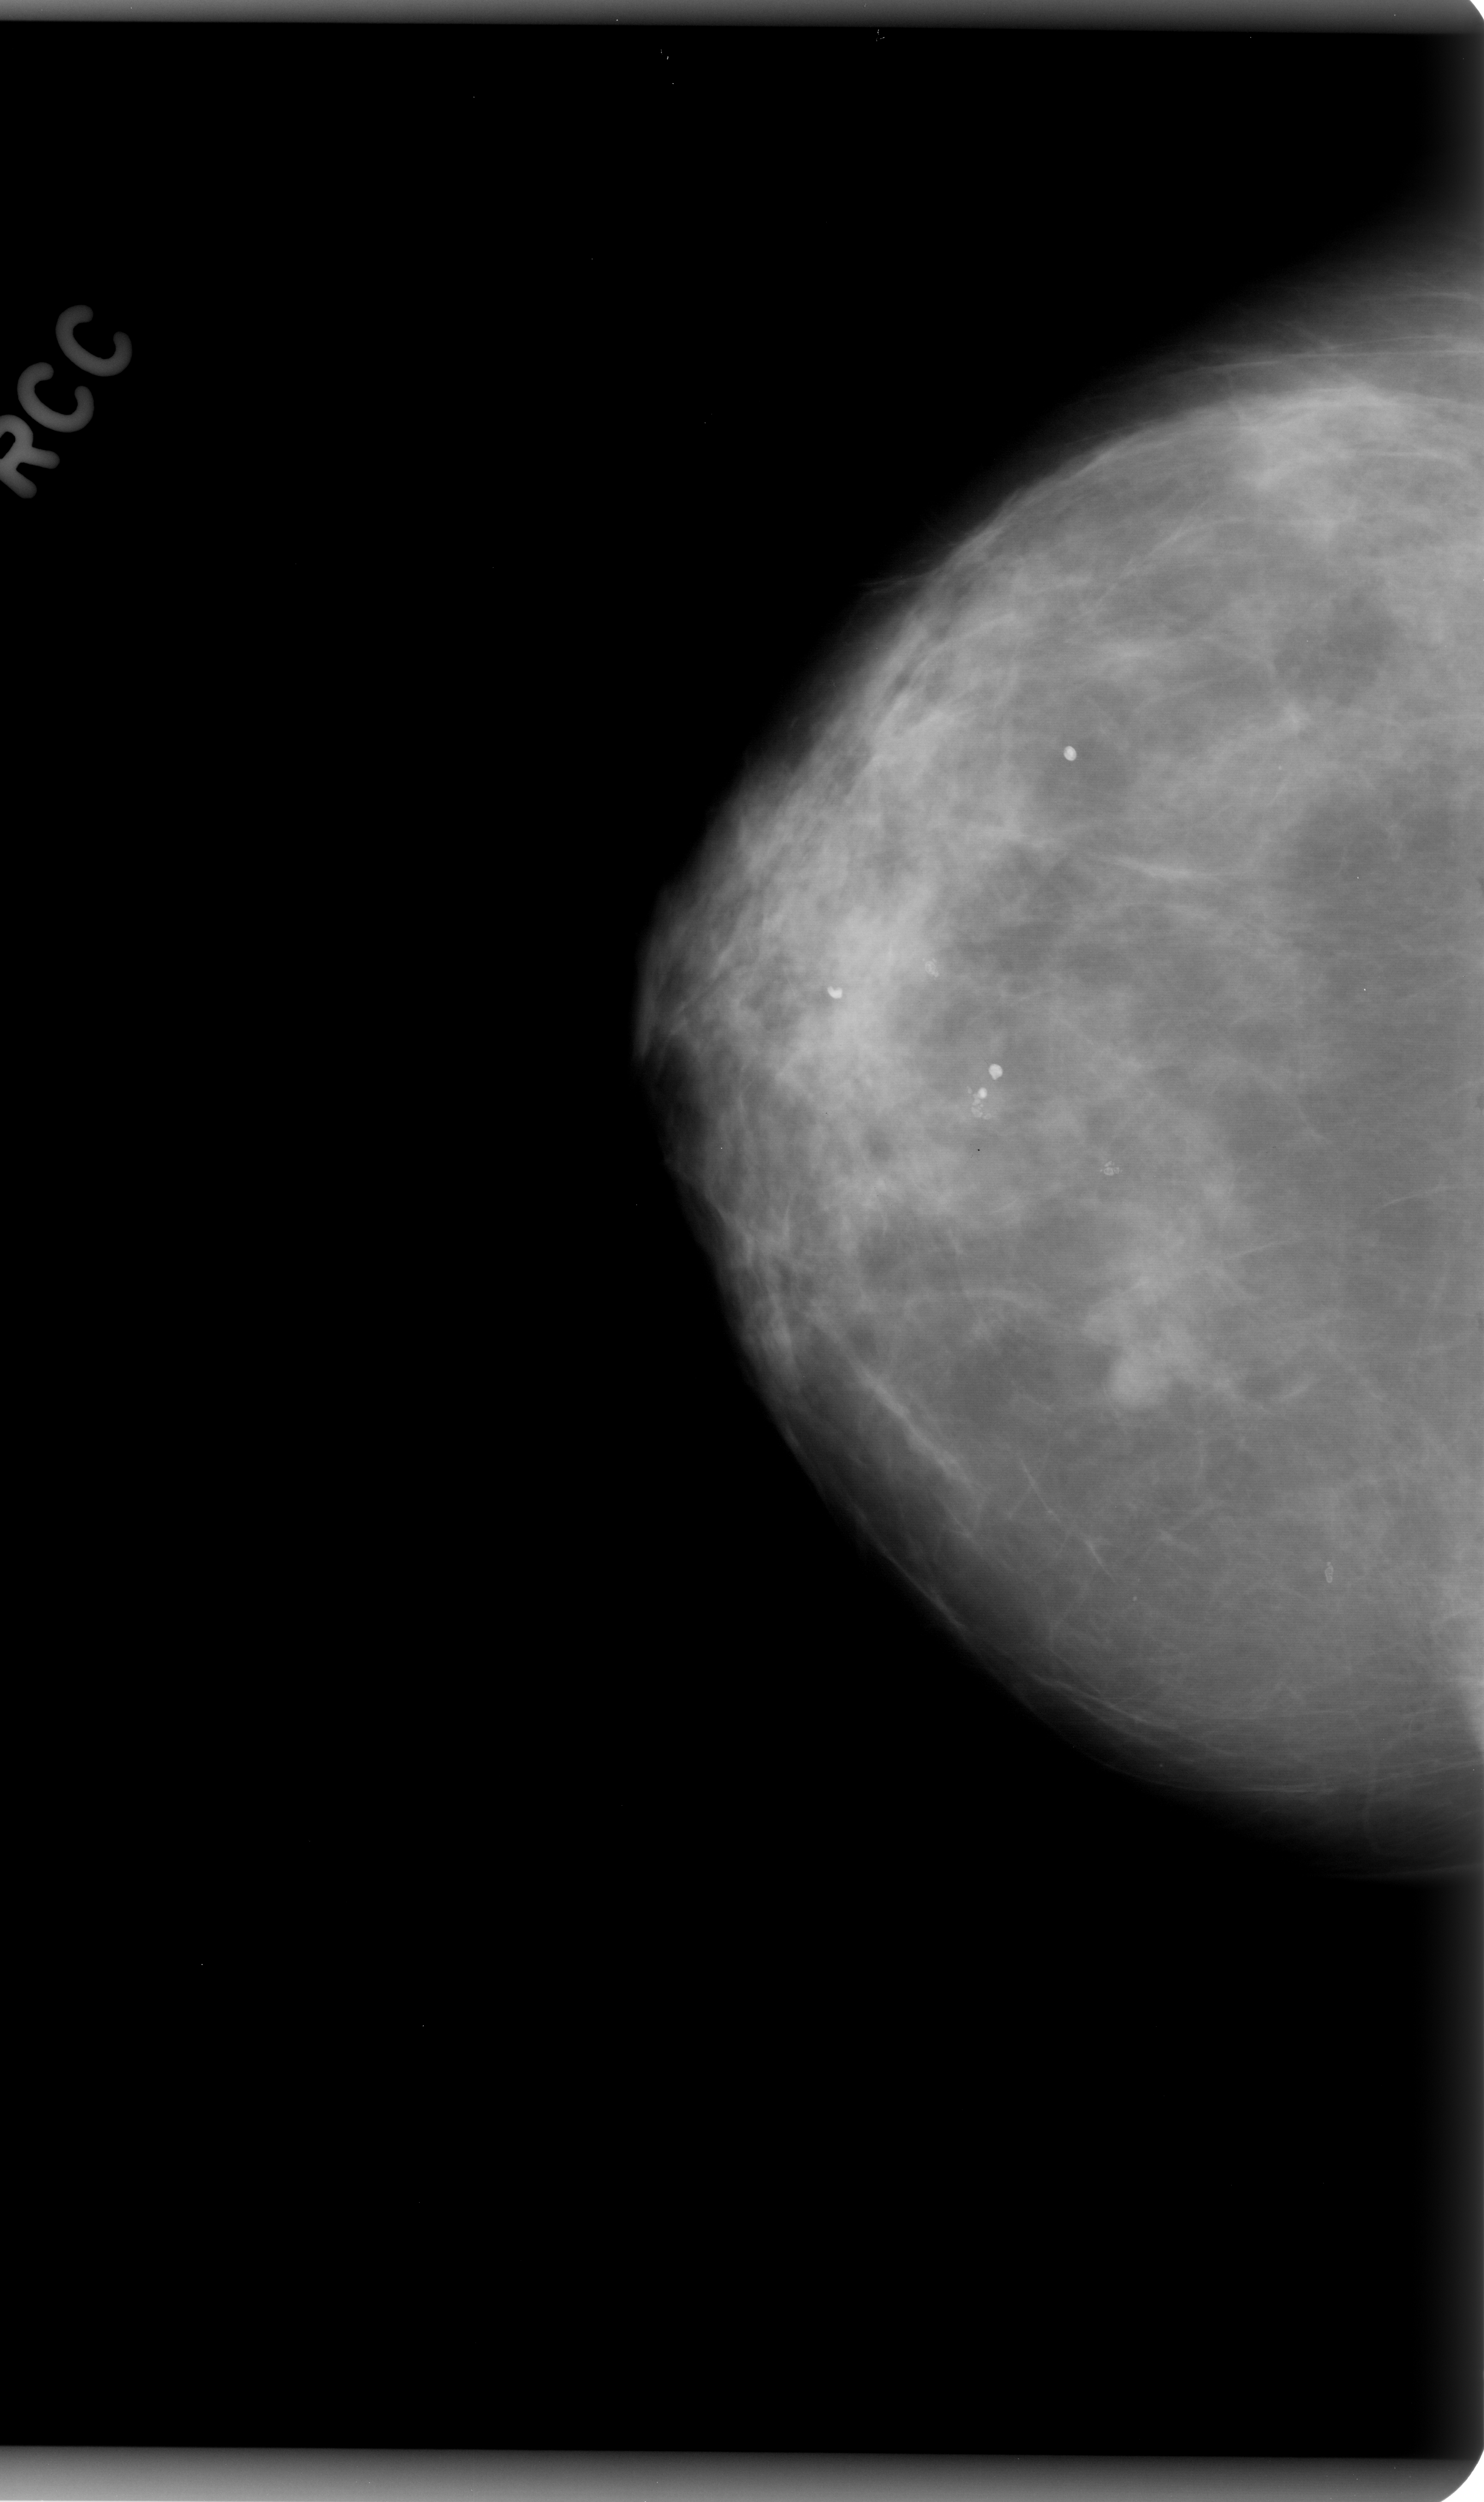
Scanned film-screen mammogram; right breast; CC view; 1484 × 2502 image matrix.
Expert-marked regions of interest on this film, with their recorded descriptors:
- mass, shape round, margins circumscribed; BI-RADS assessment category 3; pathology (as recorded): benign: bounding box [x1, y1, x2, y2] px = [1081, 1263, 1205, 1409]